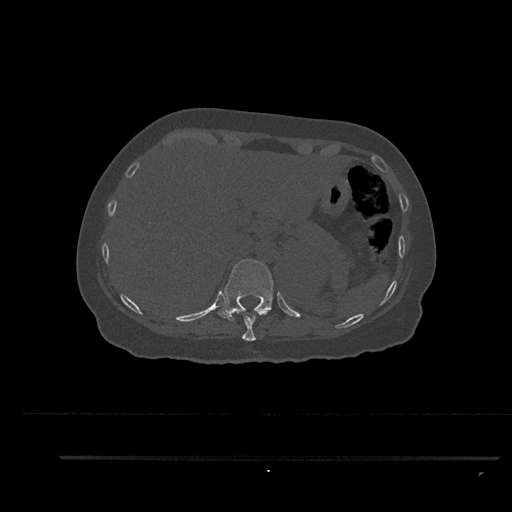
CT including the spine, one axial slice; slice 333 of 797 in the series (ordered by position); reconstruction kernel Br40s/3; 120 kVp; bone window (W 1800 / L 400 HU); 0.5 mm slice thickness; 512 × 512 image matrix, field of view 408 × 408 mm. Patient: female, 44 years. From the clinical record (not read from this slice): primary cancer: renal.
Outlined on this slice (semi-automatic segmentation, software-assisted and operator-edited):
- T10 vertebra: bounding box (x1, y1, x2, y2) in pixels: (241, 308, 256, 341)
- T11 vertebra: (217, 259, 274, 322)